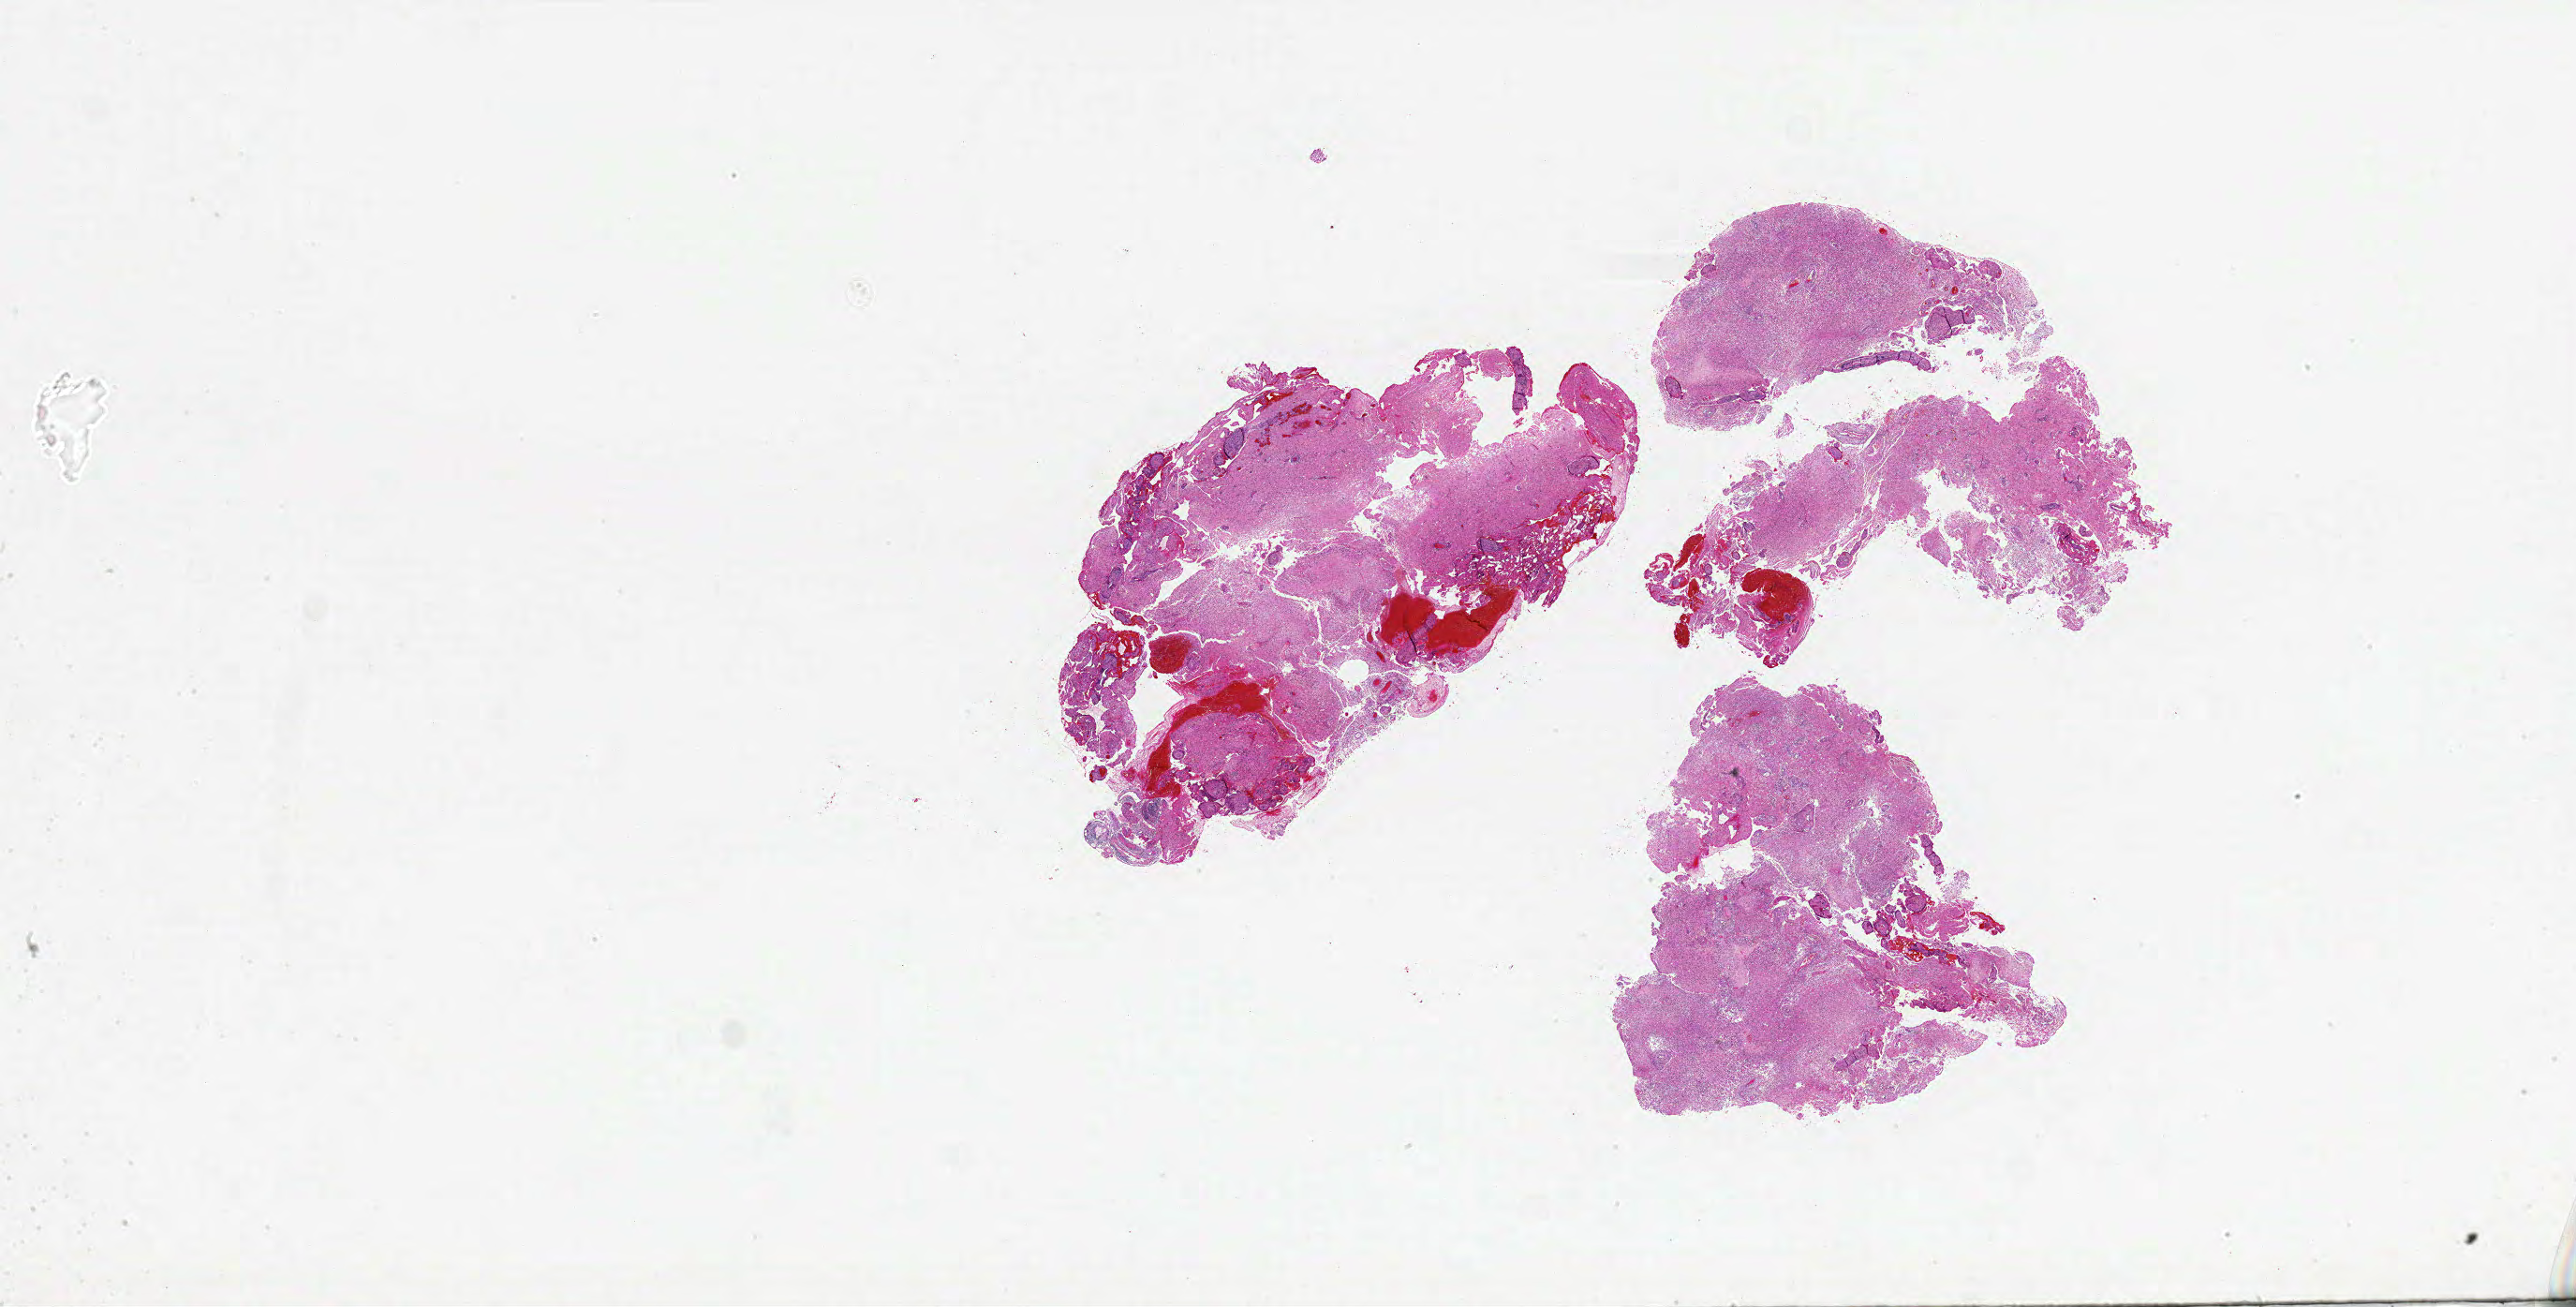
Whole-slide histology image, H&E, whole scanned area (about 44.0 x 22.3 mm, slide scanned at 20x) shown as a low-resolution overview. Formalin-fixed paraffin-embedded (FFPE) diagnostic section. Primary tumour sample from the brain. Male patient; age at initial diagnosis 58 years.
Diagnosis: Glioblastoma.